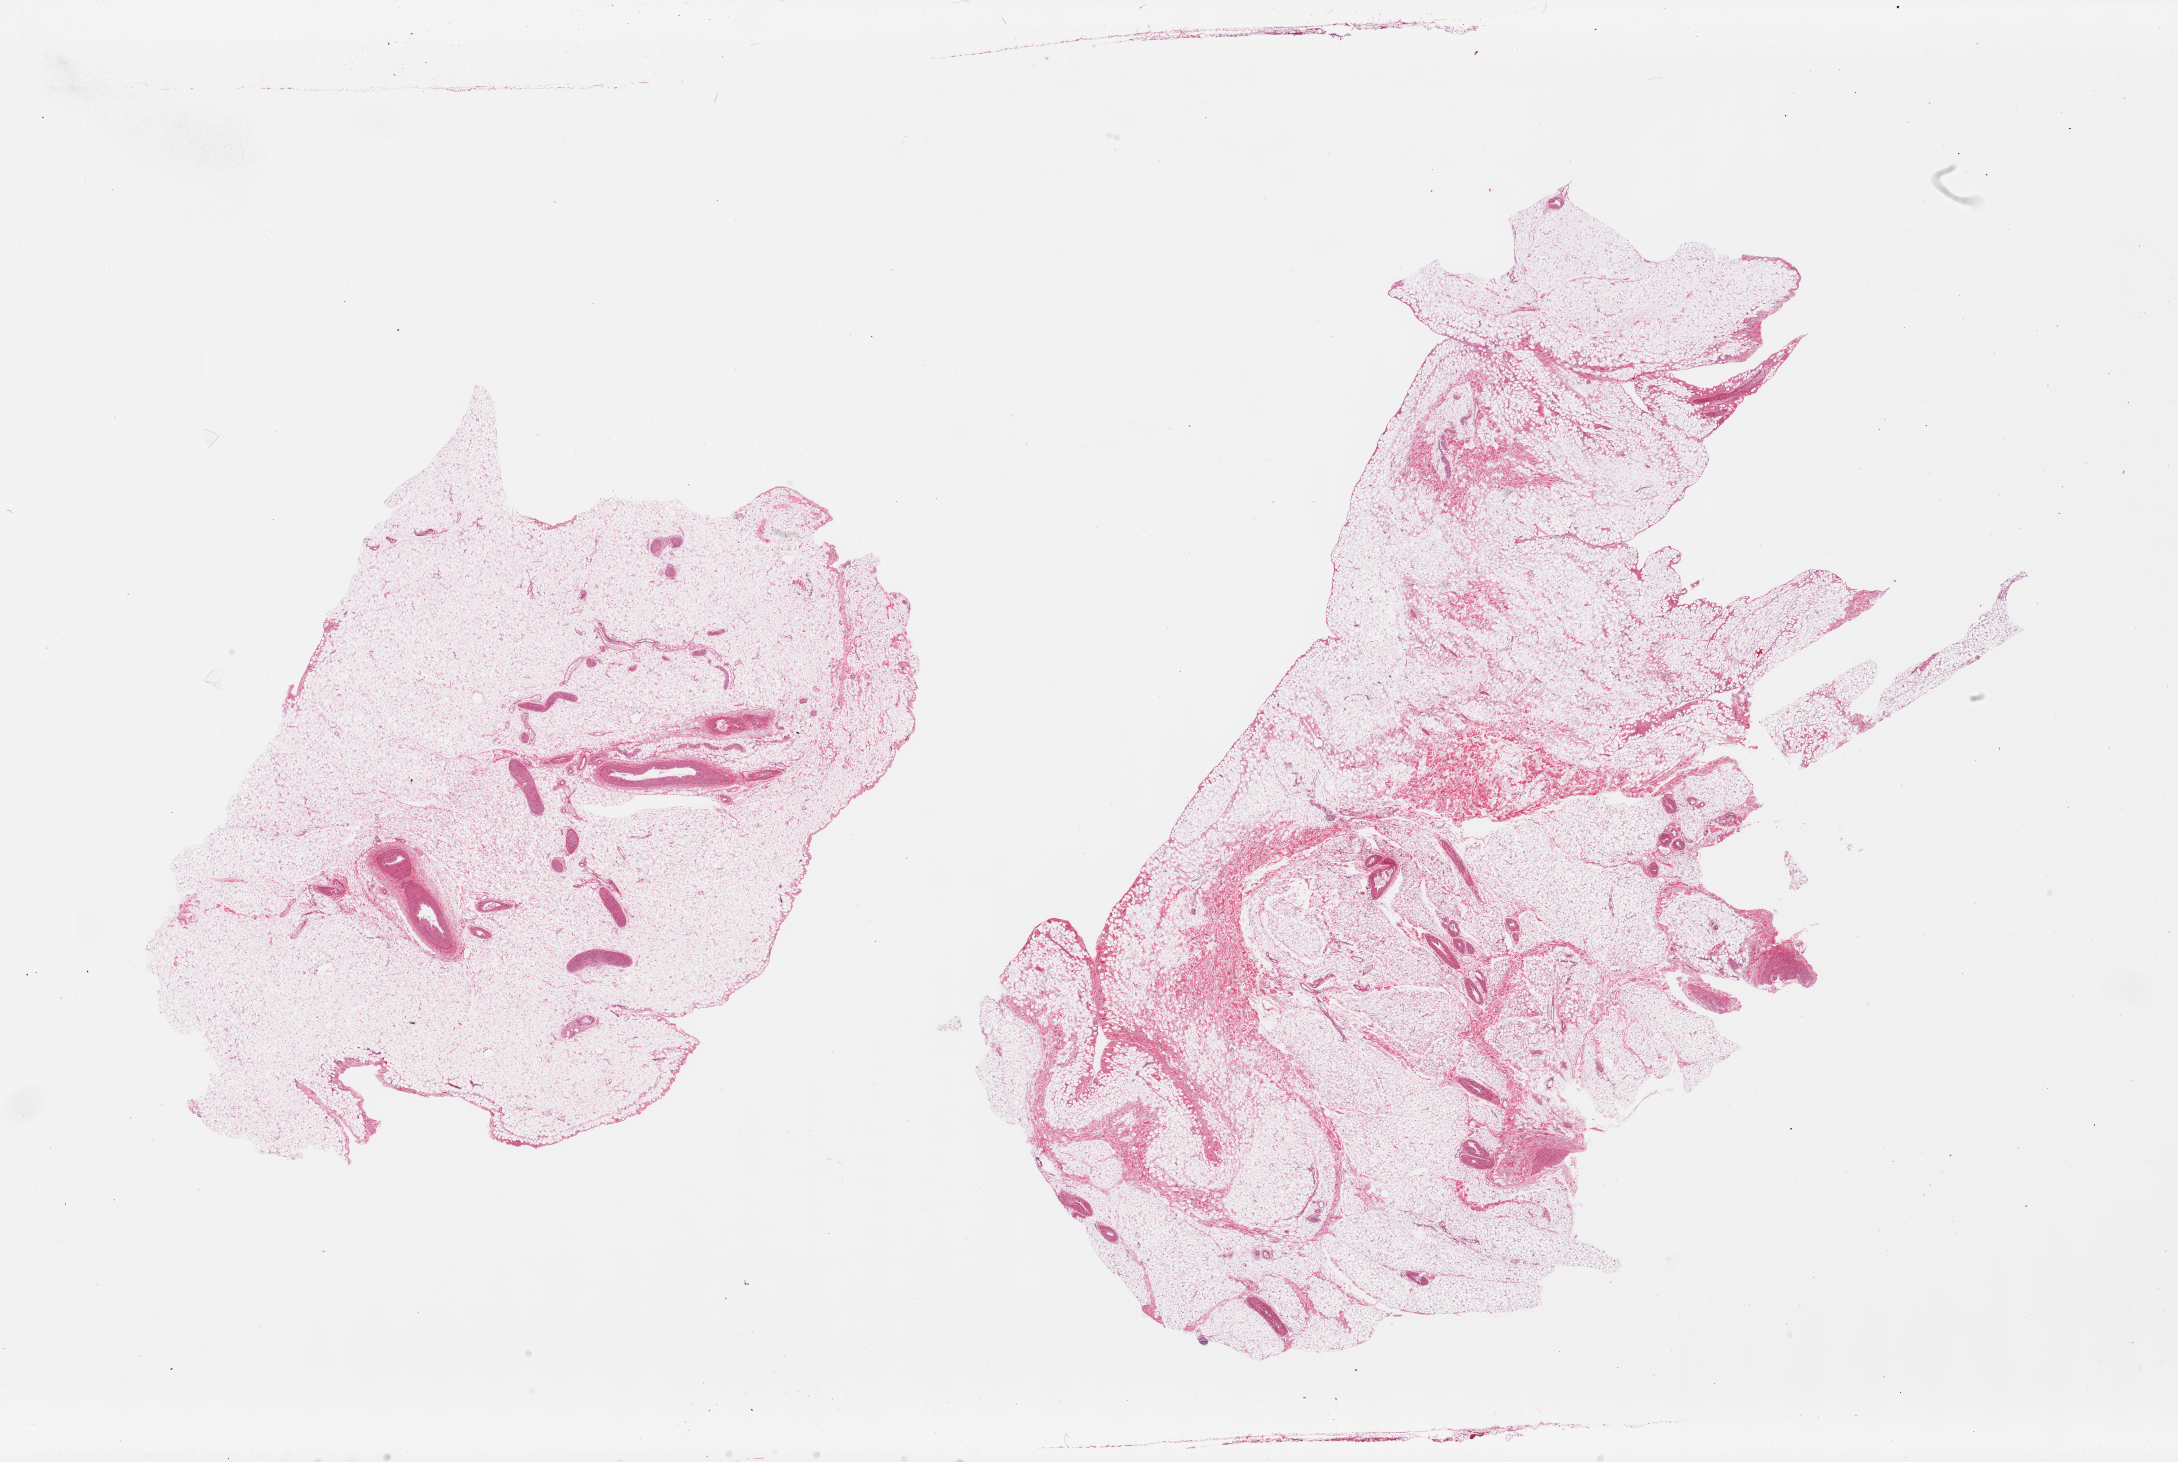
Haematoxylin and eosin whole-slide image, brightfield, shown as a low-resolution overview of the whole scanned area (about 34.5 x 23.1 mm); PAXgene-fixed paraffin-embedded (PFPE) section; target tissue: omentum; tissue donor sample. Donor: male.
* reviewer comment on this tissue sample: 2 pieces, vascular elements/fascia are ~1015% of tissue